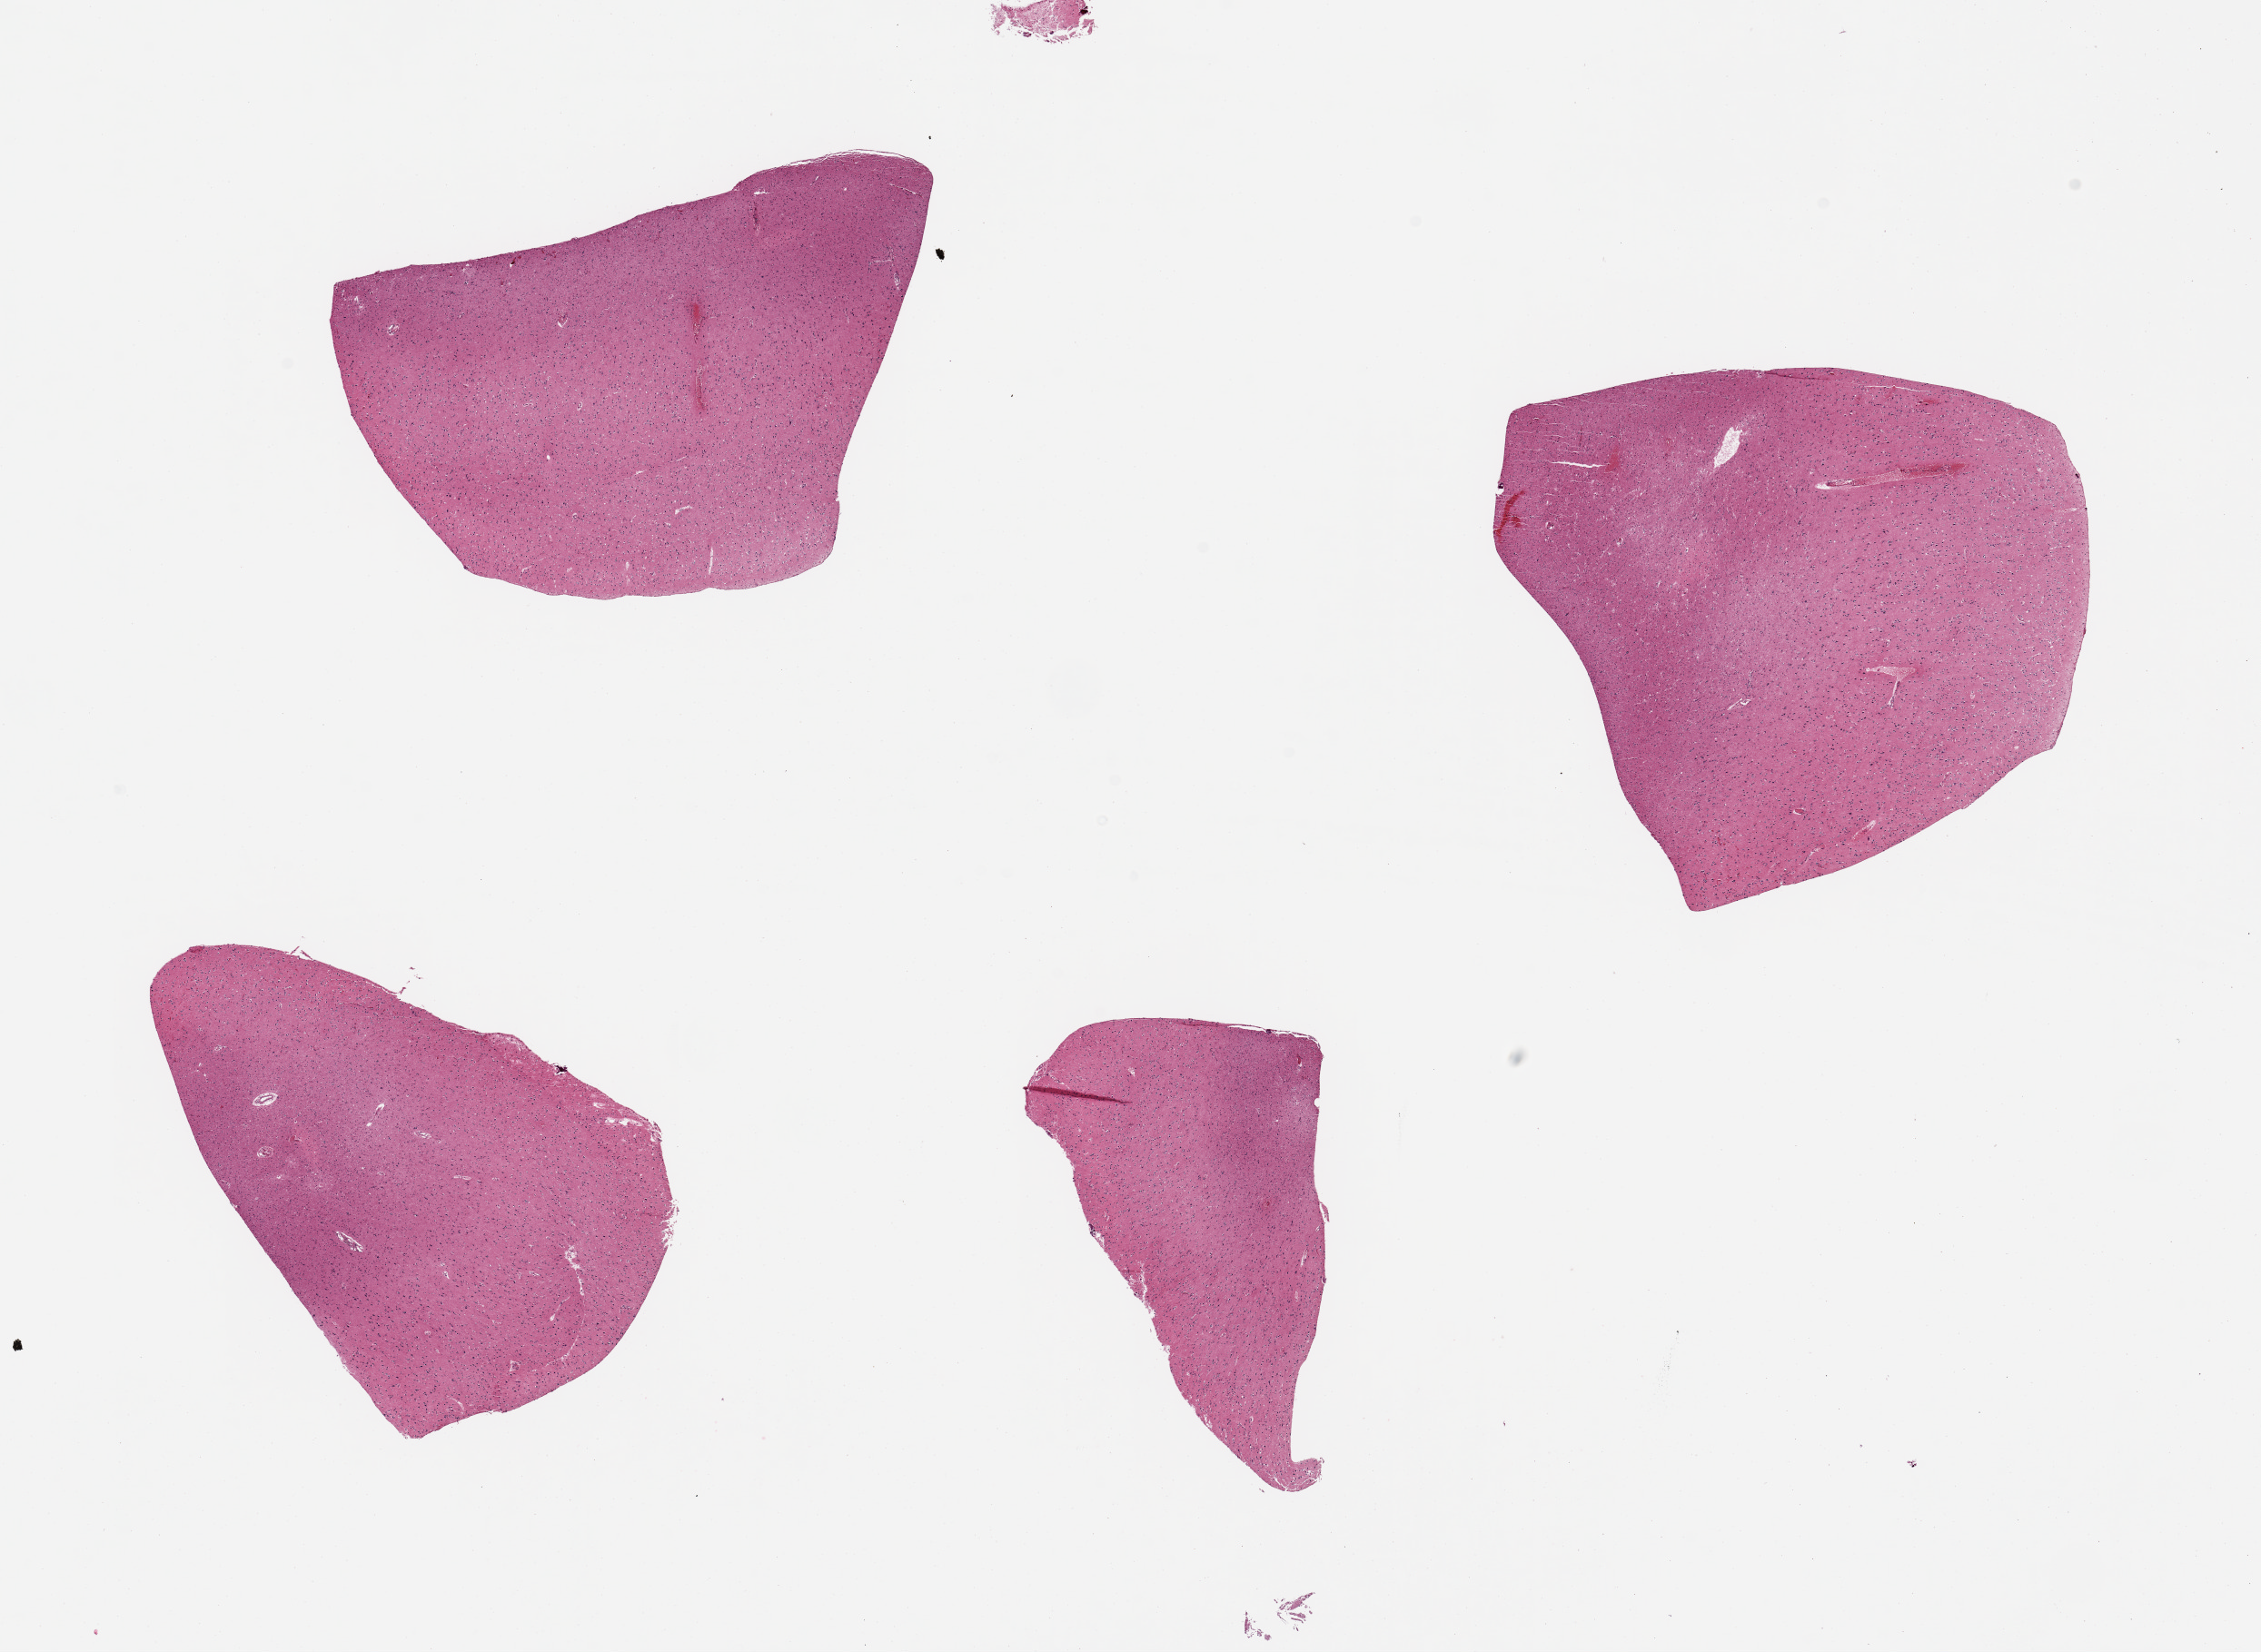
Haematoxylin and eosin whole-slide image, shown as a low-resolution overview of the whole scanned area (about 19.7 x 14.4 mm). PAXgene-fixed, paraffin-embedded tissue. Section of cerebral cortex (target tissue). Tissue donor sample. Donor: male.
Reviewer comment on this tissue sample: 4 pieces.